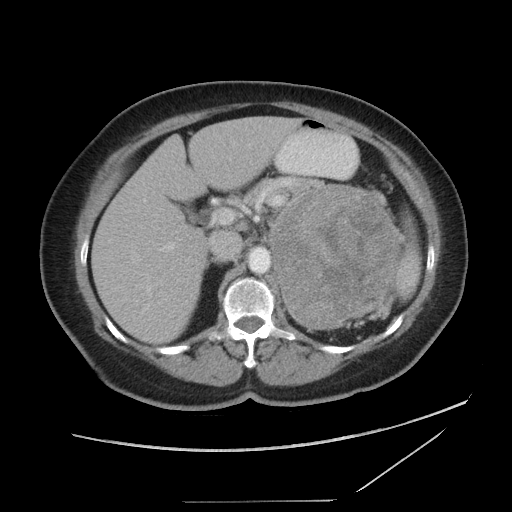
Contrast-enhanced abdominal CT, one axial slice. Position 58 of 86 along the scan axis. Reconstruction kernel STANDARD. 120 kVp. Intravenous contrast given. Soft-tissue window (W 400 / L 40 HU). 5 mm slice thickness. 512 × 512 image matrix, field of view 398 × 398 mm. Female patient, age 77 years. Case-level facts recorded for this patient, not image findings: diagnosis: adrenocortical carcinoma; tumour side: left adrenal; tumour size at pathology: 13.1 cm; Ki-67 index: 10 %; stage (as recorded): 3.
Annotated regions visible in this slice (semi-automatically segmented with operator editing):
- mass: bounding box <273,185,398,328> (left, top, right, bottom; pixels)